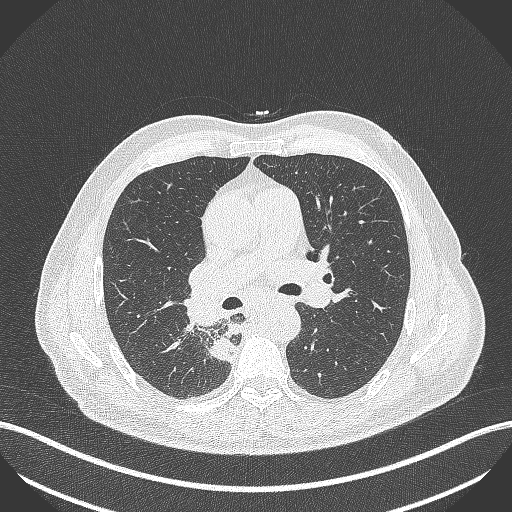
Chest CT, one axial slice. Position 274 of 451 along the scan axis. Reconstruction kernel B70f. 100 kVp. Lung window (W 1500 / L -600 HU). 1 mm slice thickness. 512 × 512 image matrix, field of view 400 × 400 mm. Male patient, age 61 years. From the clinical record (not read from this slice): clinical TNM (as recorded): T1 N0 M0; histopathological grade: G3.
Annotated regions visible in this slice (rectangle marked by the reading radiologist):
- lung tumour (recorded histology: small cell carcinoma): box from (x=205, y=332) to (x=238, y=366) px